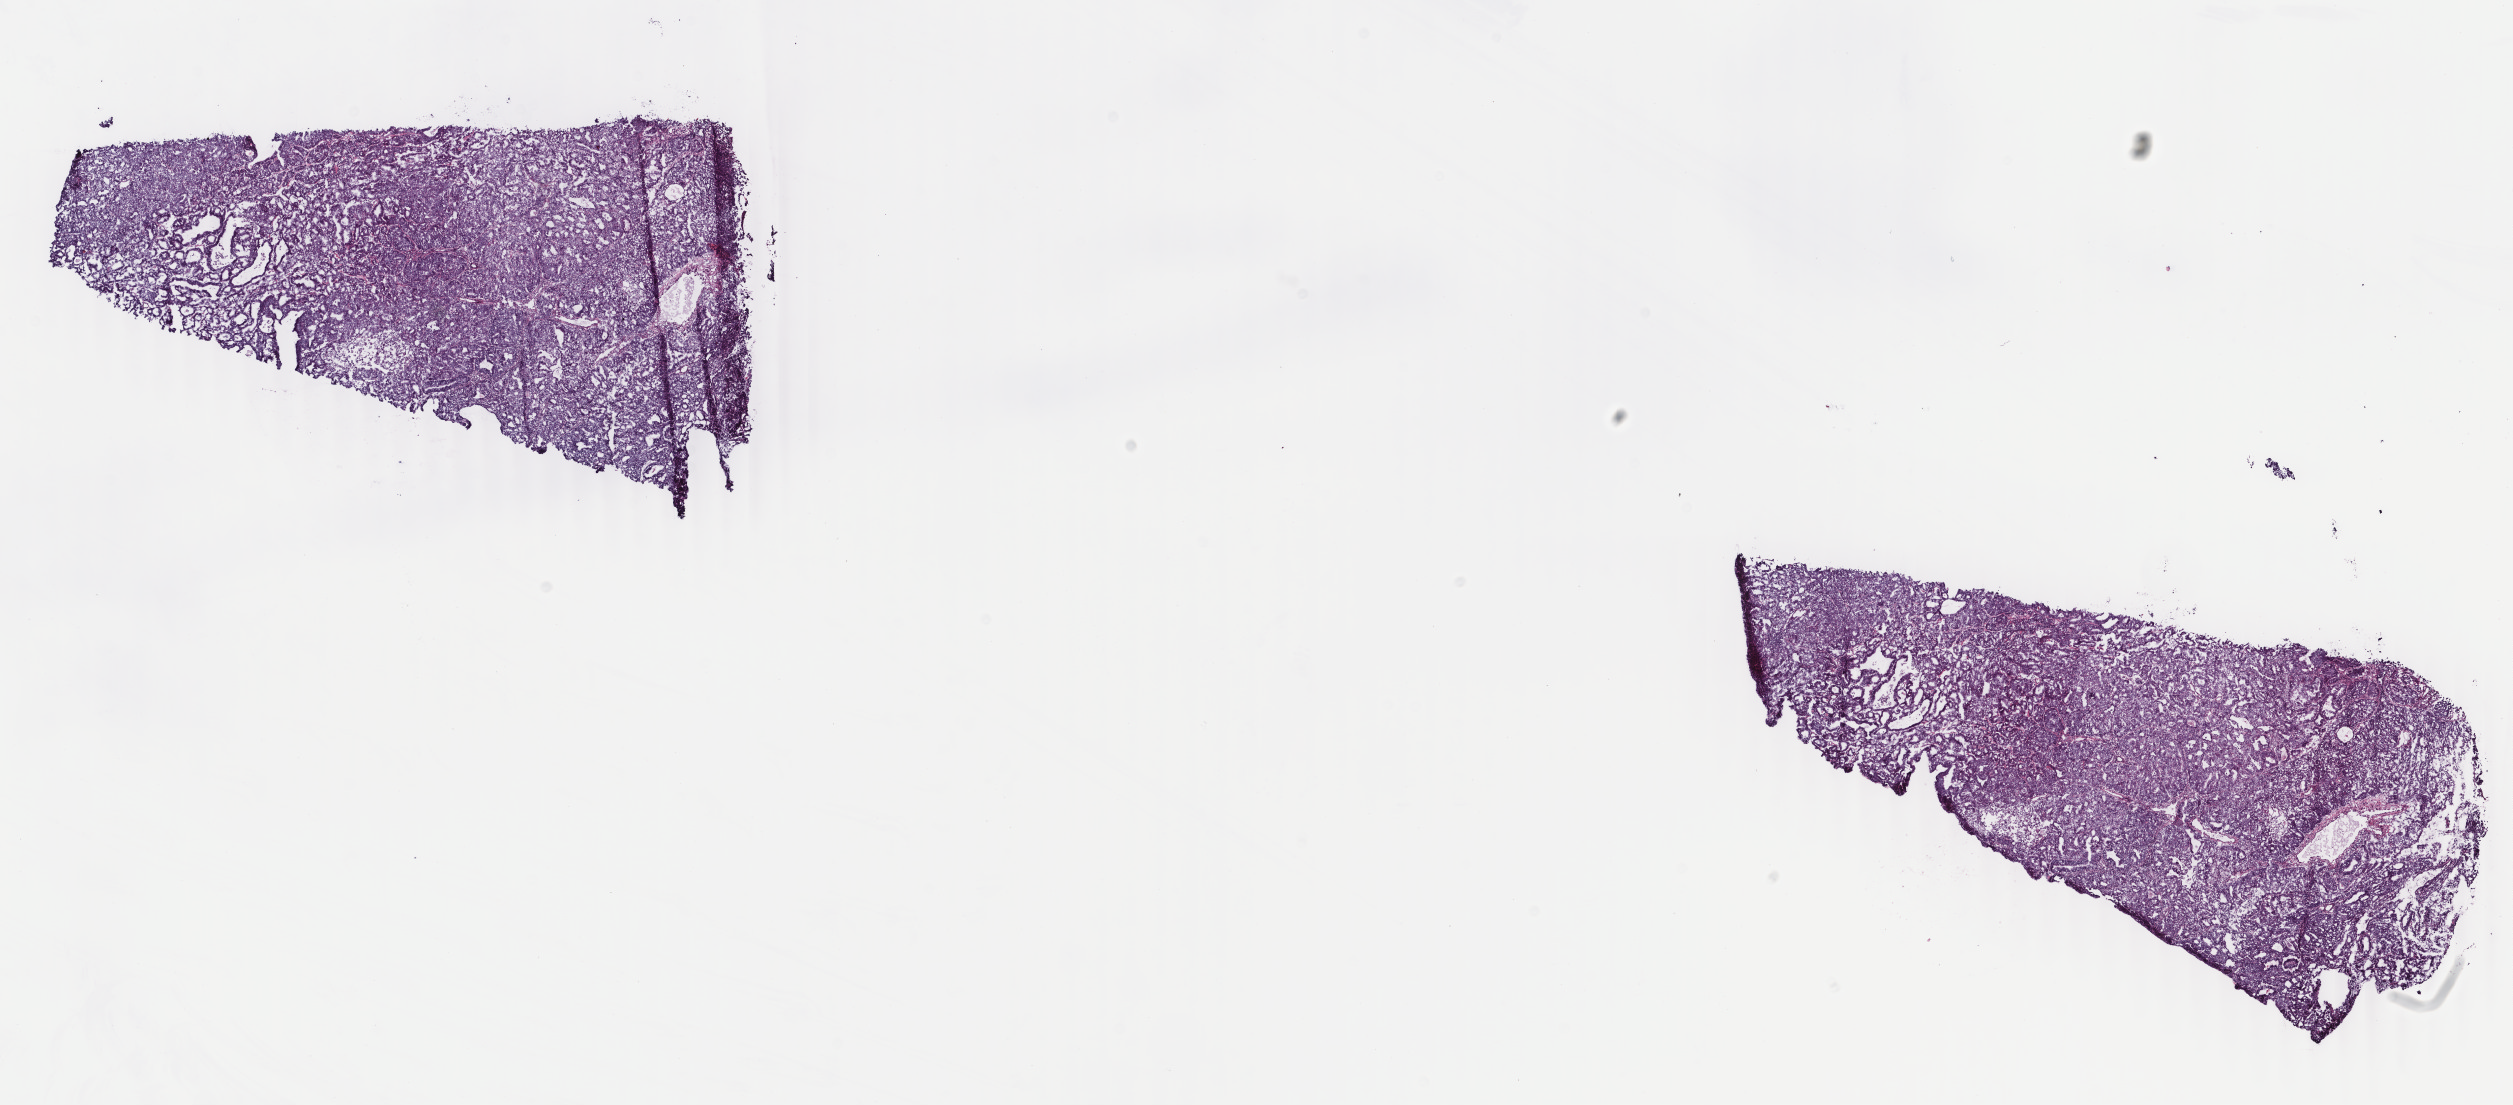
Digitized H&E tissue section (whole slide) — a low-resolution overview of the entire scanned area, about 20.0 x 8.8 mm, frozen section, primary tumour sample from the uterus. Patient: female, age at initial diagnosis 67 years.
Pathologic diagnosis: Endometrioid adenocarcinoma, NOS (endometrium).